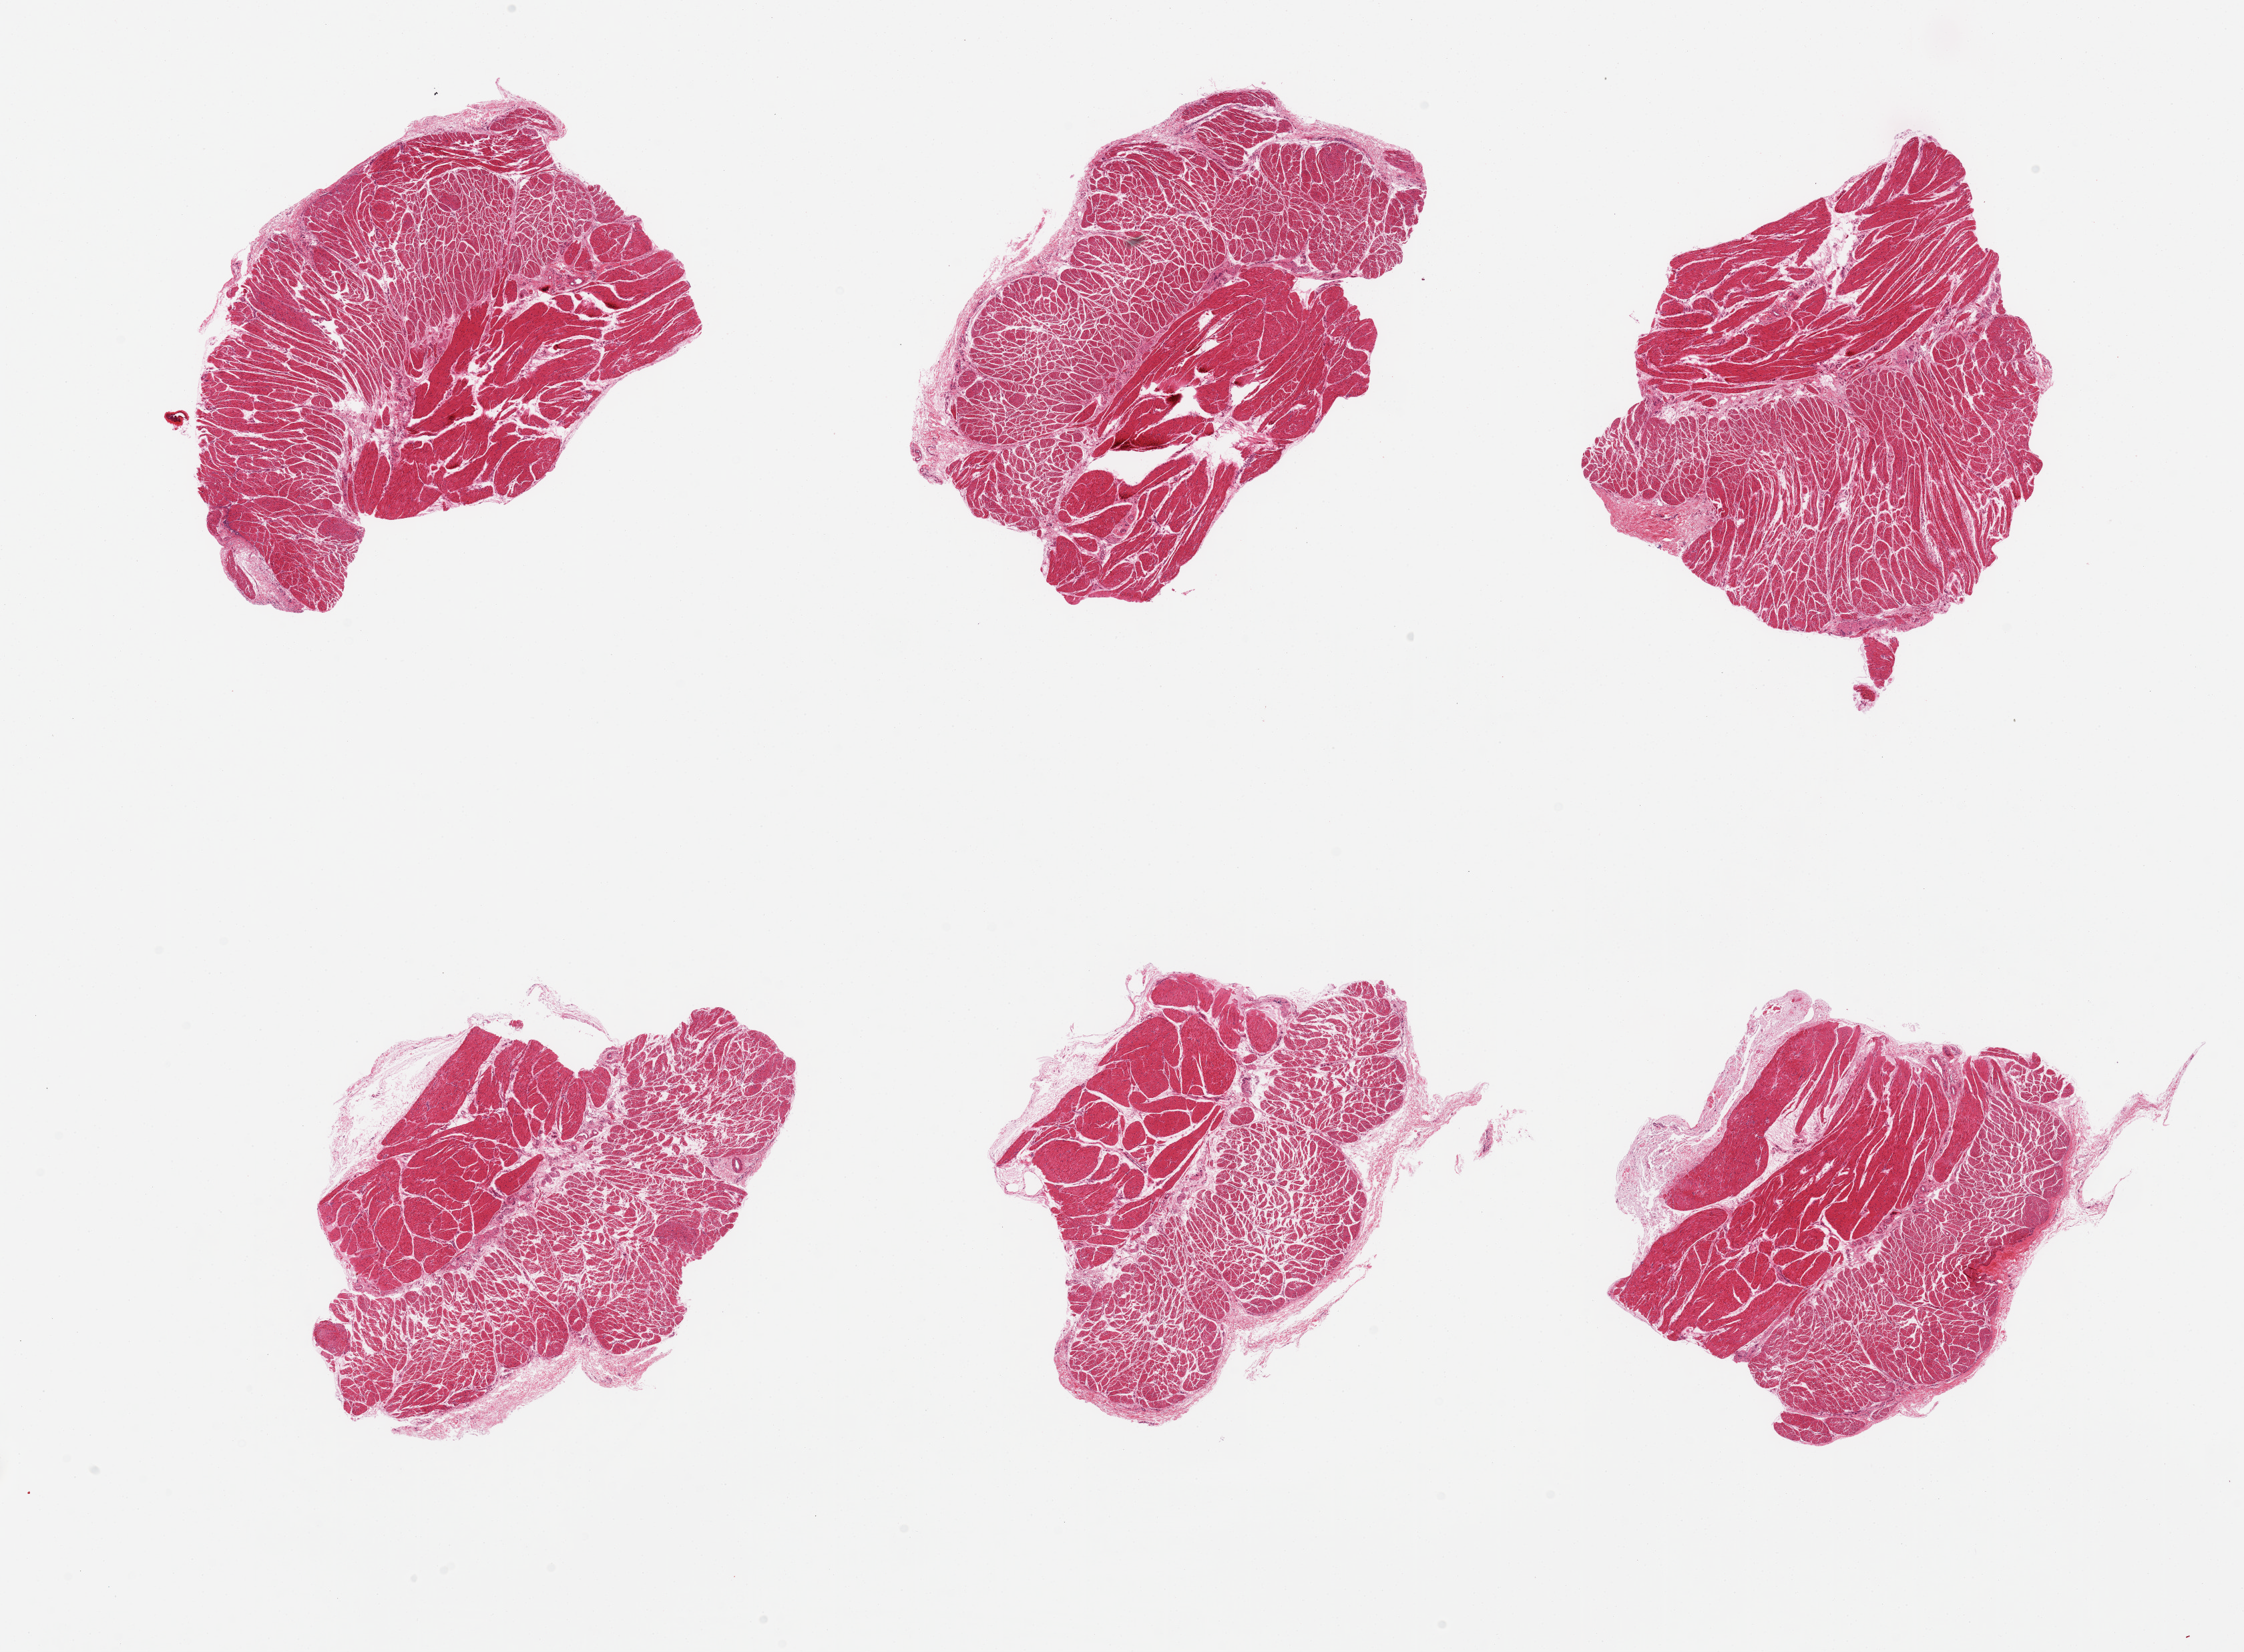
Whole-slide image, H&E stain, brightfield — low-resolution overview of the scanned area, about 26.6 x 19.6 mm. PAXgene-fixed, paraffin-embedded tissue. Target tissue: esophageal muscle. Donor tissue sample. Donor: male.
Reviewer comment on this tissue sample: 6 pieces, all muscularis, good specimens.